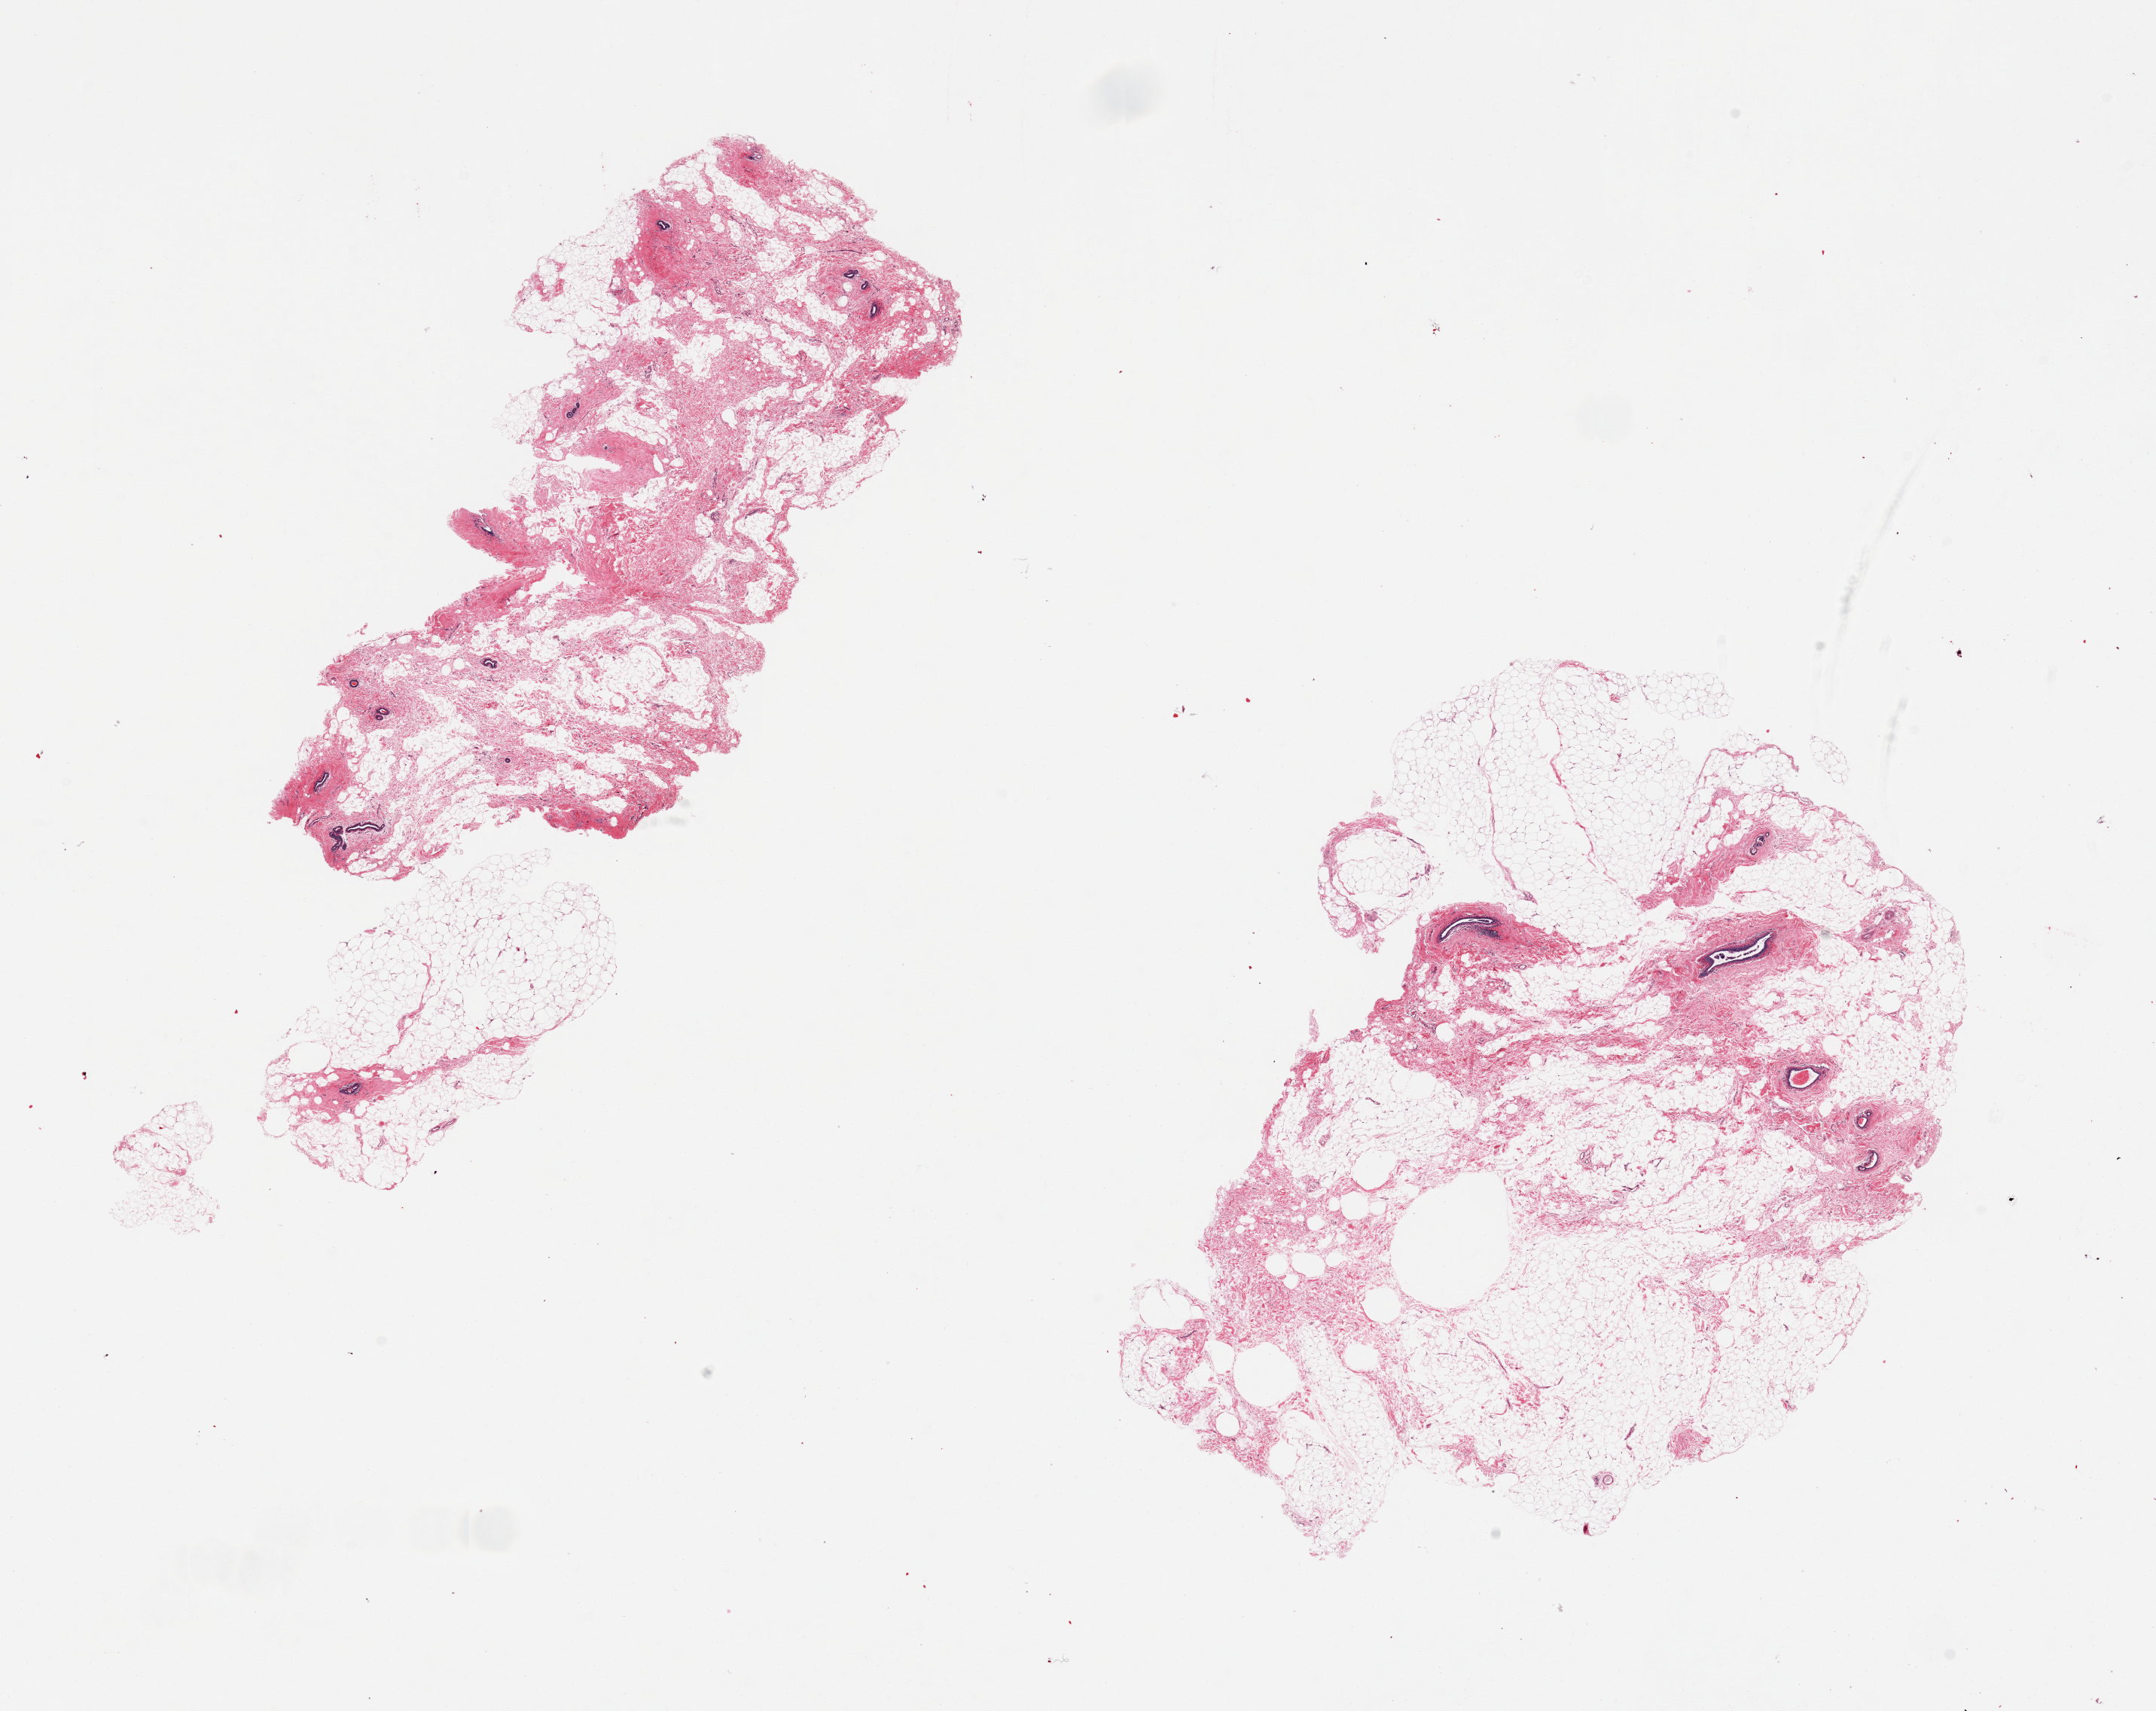
Whole-slide image, H&E stain — low-resolution overview of the scanned area, about 22.6 x 18.0 mm (acquisition: 20x scan), PAXgene-fixed, paraffin-embedded tissue, target tissue: breast, tissue donor sample.
Pathologist's review note for this sample: 2 pieces, fibrofatty tissue, epithelium represents <5%.